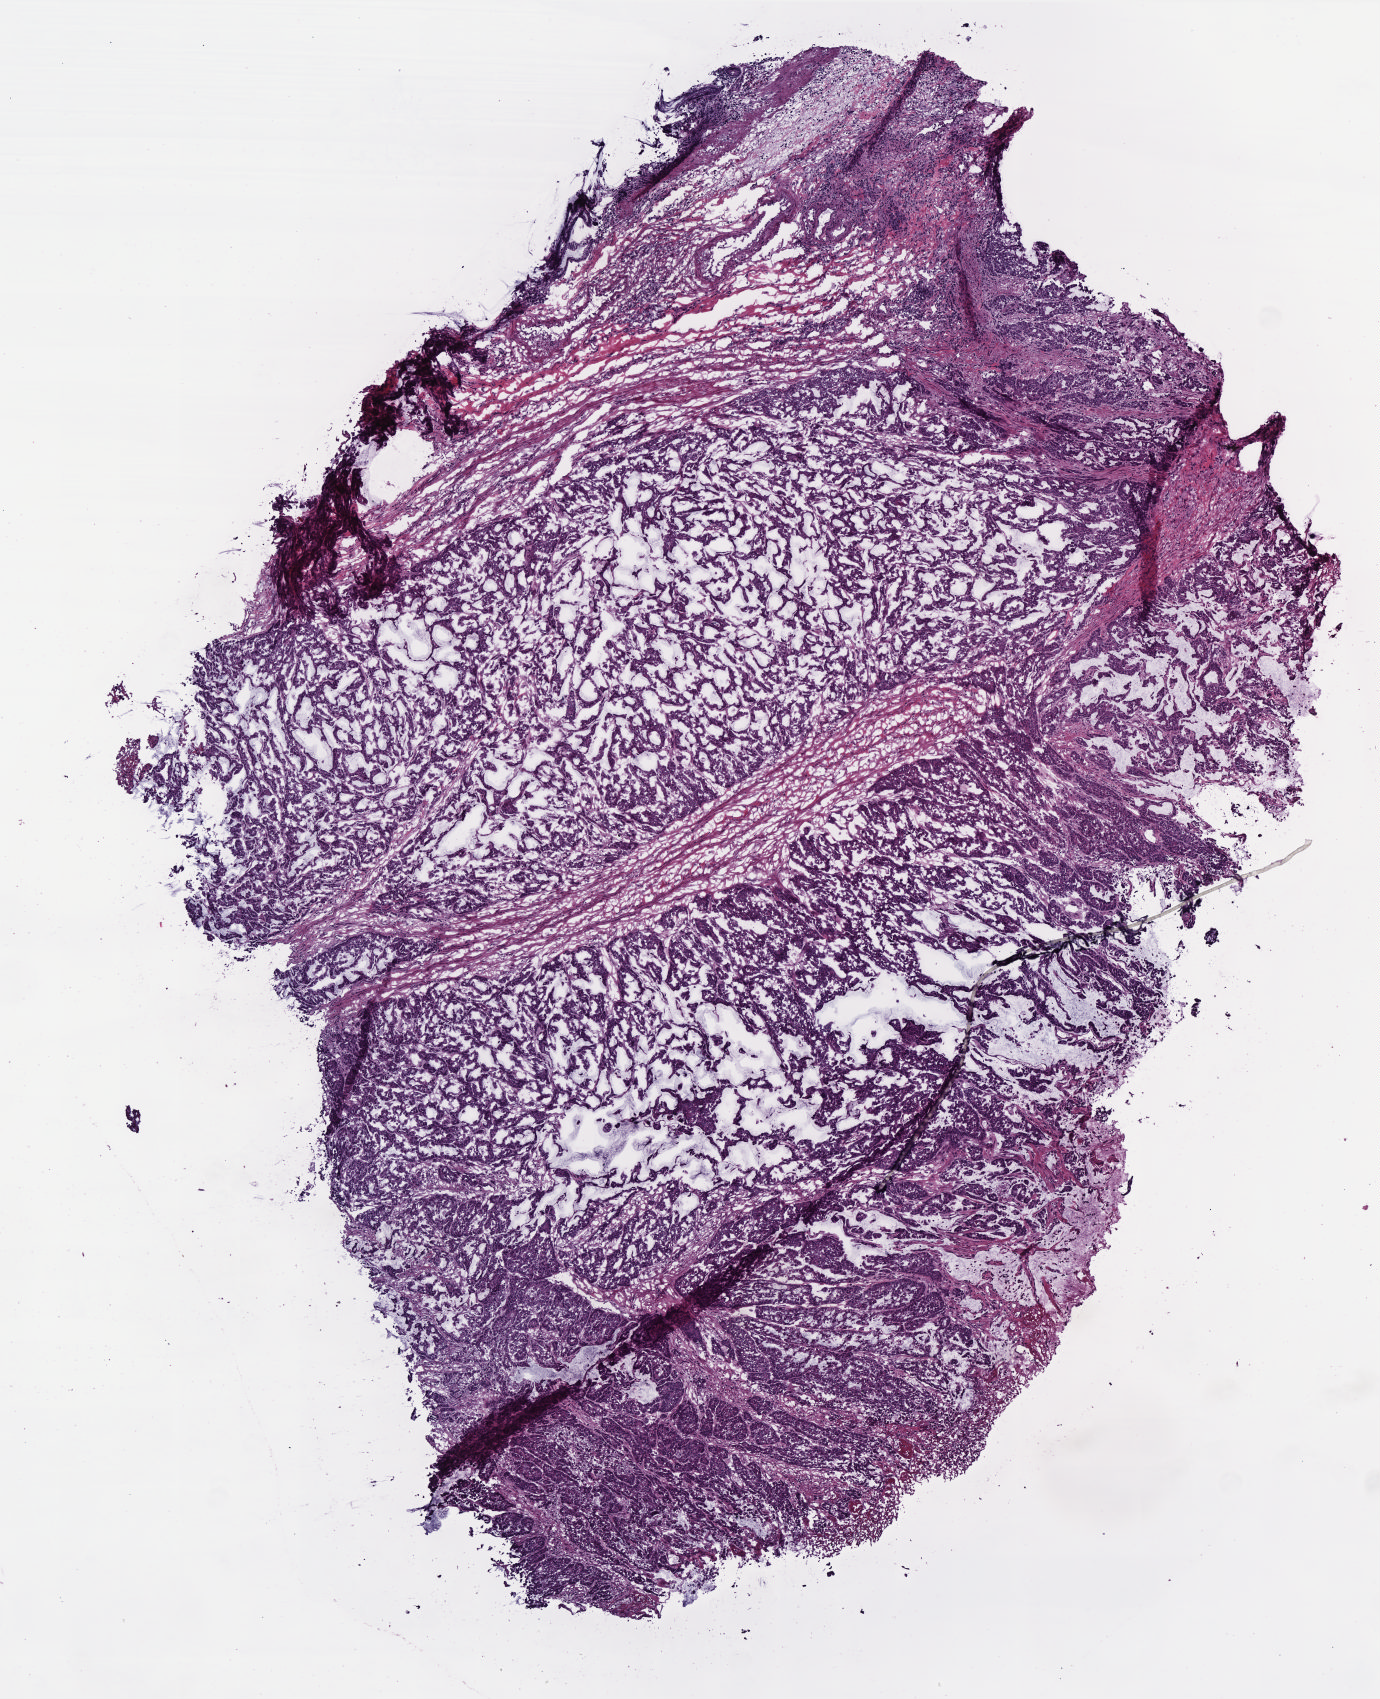
Digitized H&E tissue section (whole slide) — low-resolution overview of the scanned area, about 5.5 x 6.8 mm (from a 40x scan); frozen section; colon, primary tumour sample. Patient: male, age at initial diagnosis 80 years. Slide review estimates, as recorded: tumour cells 85%, tumour nuclei 95%, normal cells 0%, stromal cells 14%, necrosis 1%. Inflammatory infiltration, as recorded: lymphocyte infiltration 2%, monocyte infiltration 1%, neutrophil infiltration 0%.
Lymph nodes positive (case pathology): 2 of 24 examined. AJCC pathologic stage: IIIB (6th edition). Diagnosis: Mucinous adenocarcinoma. TNM: T4 N1 M0.